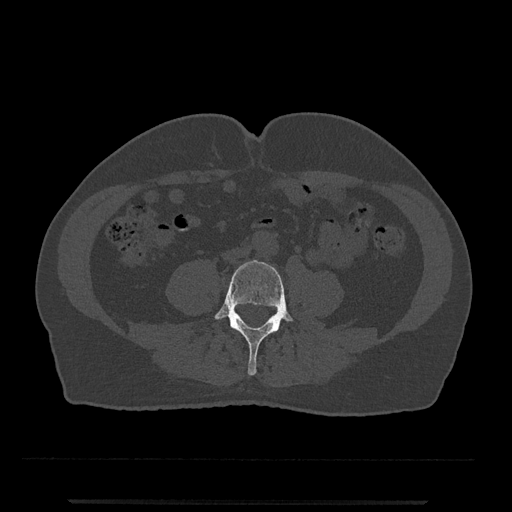
CT including the spine, one axial slice. Position 136 of 797 along the scan axis. Bone window (W 1800 / L 400 HU). 0.5 mm slice thickness. 512 × 512 image matrix, field of view 419 × 419 mm. Patient: male, 63 years. Case-level facts recorded for this patient, not image findings: primary cancer: prostate.
Outlined on this slice (semi-automatic segmentation, software-assisted and operator-edited):
- L4 vertebra: bounding box (x1, y1, x2, y2) in pixels: (213, 260, 294, 376)